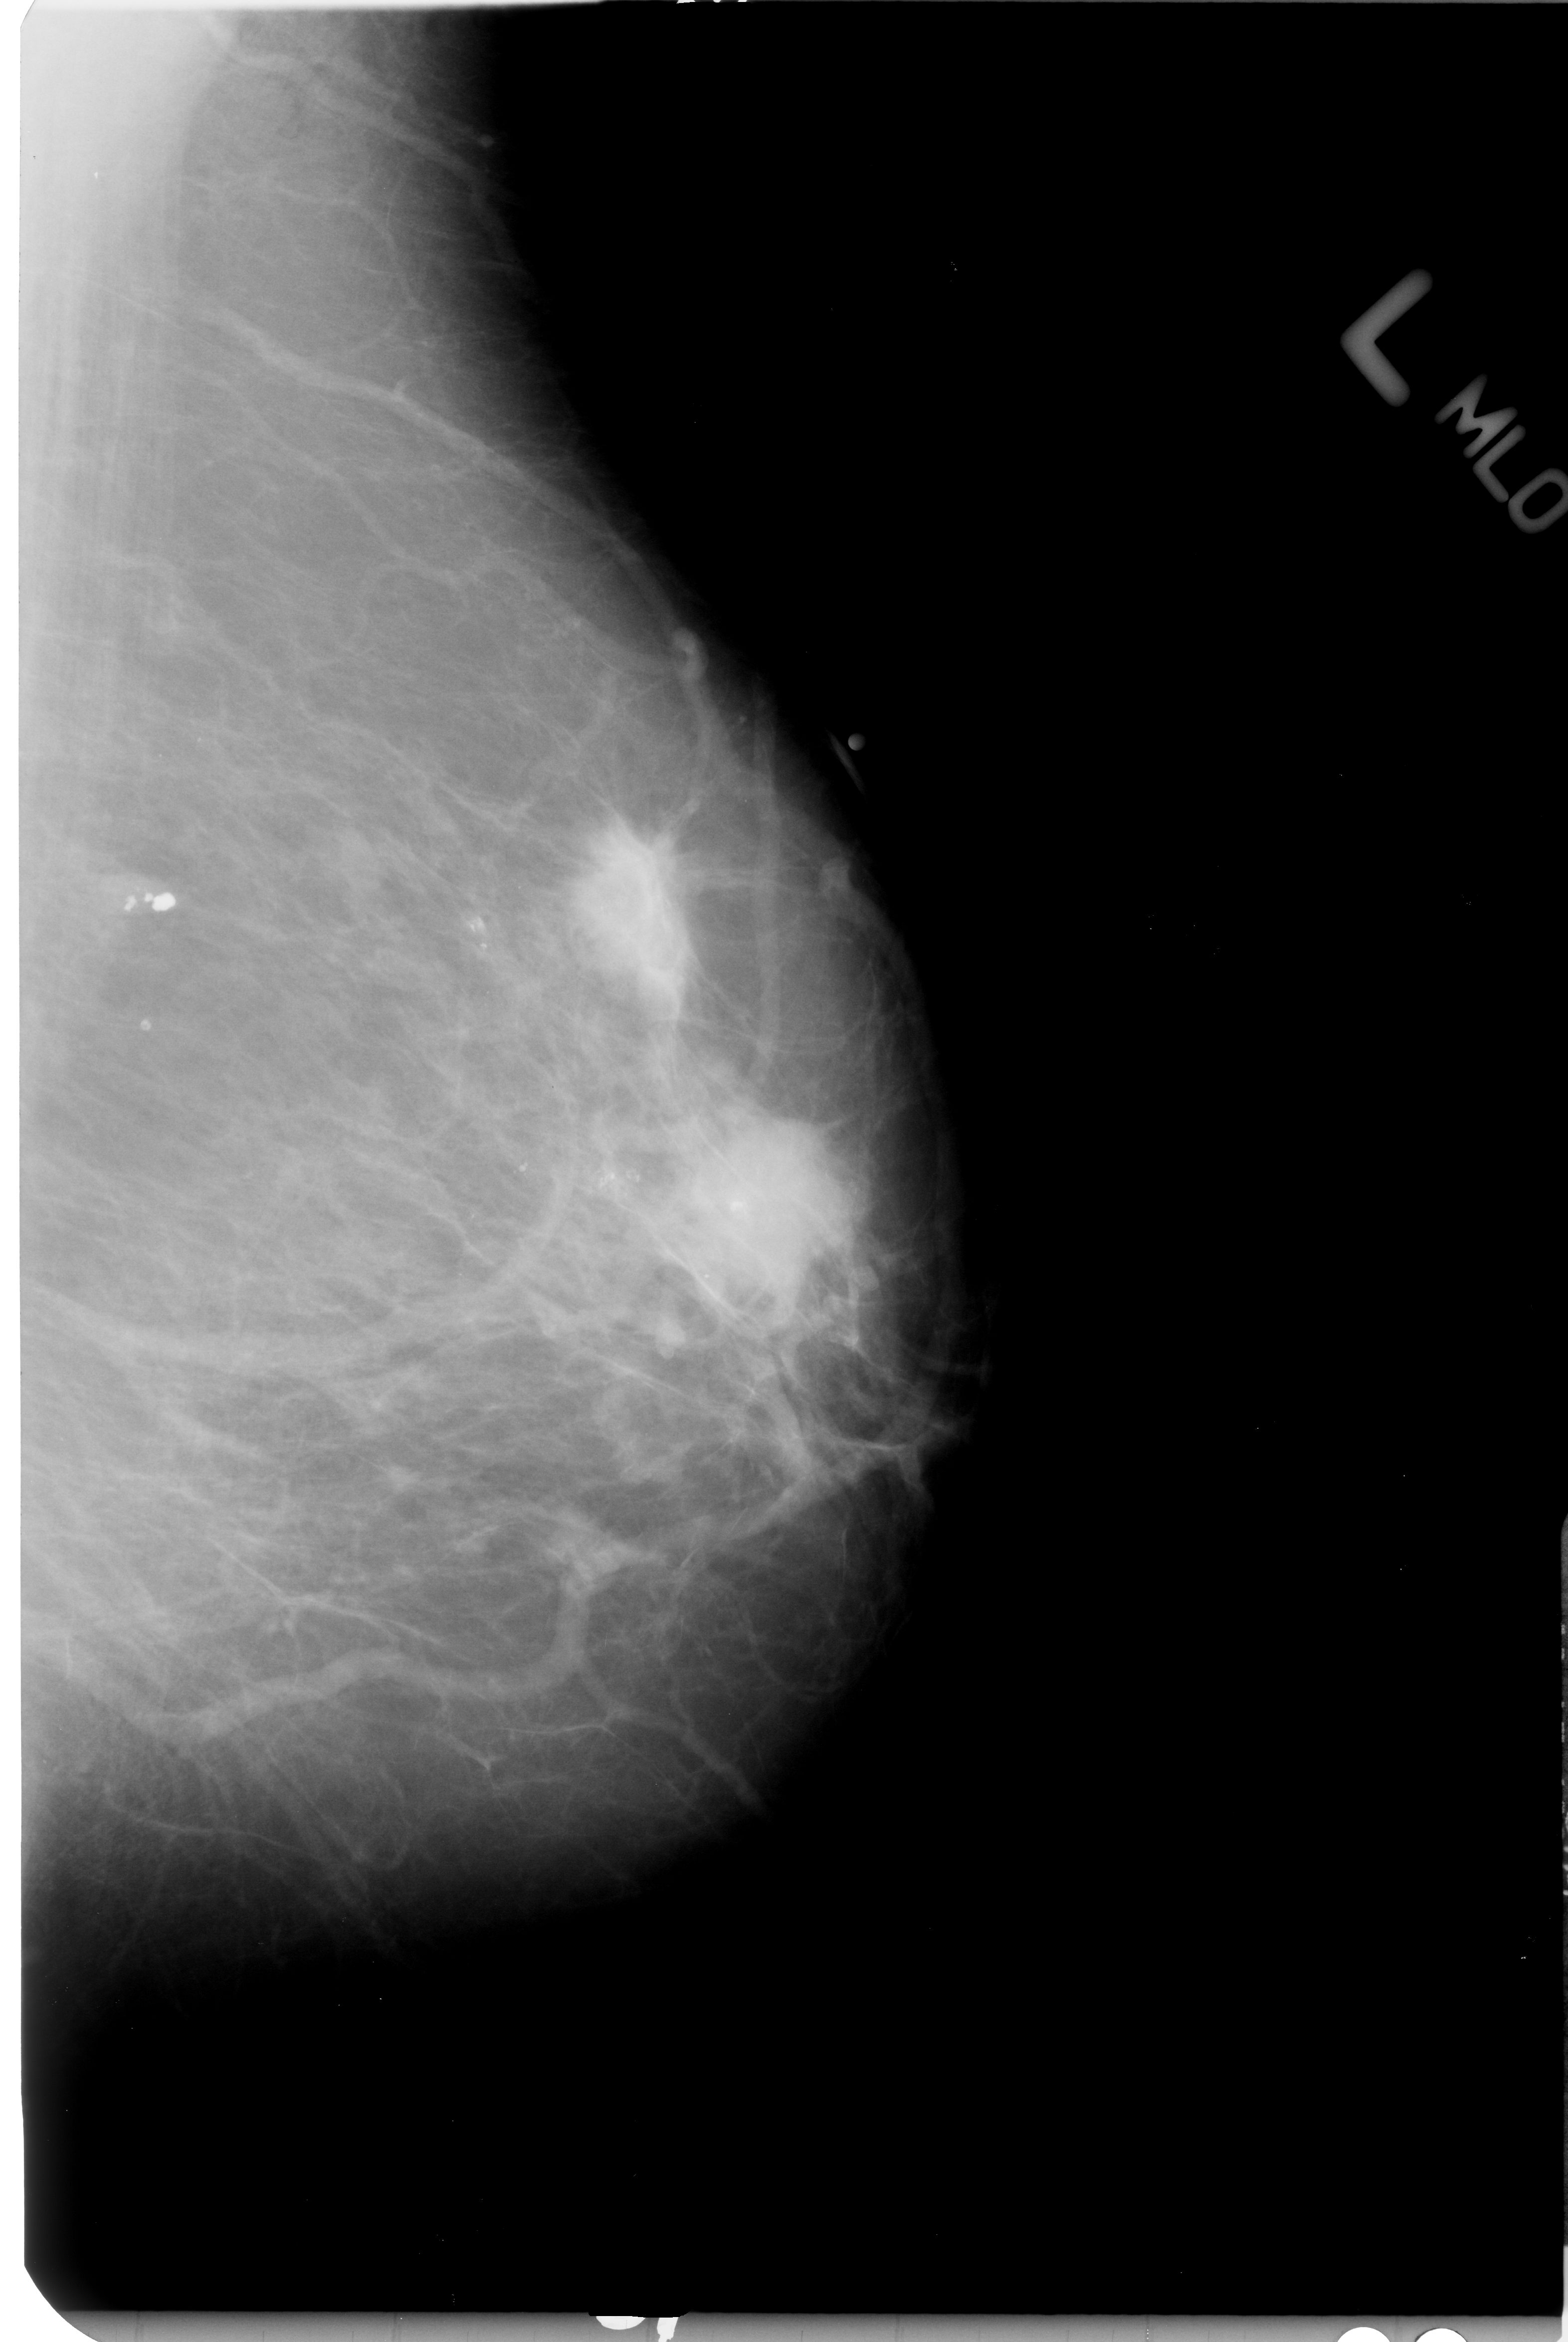
Digitized screen-film mammogram; left breast; MLO view; BI-RADS breast density category 2 (scale 1–4); 1568 × 2342 image matrix.
Expert-marked regions of interest on this film, with their recorded descriptors:
- Finding 1 of 2: mass, shape irregular / architectural distortion, margins spiculated; BI-RADS assessment category 5; subtlety rating 5 on a 1 (subtle) to 5 (obvious) scale; pathology result (as recorded, not read from the image): malignant: bounding box <560,800,714,991> (left, top, right, bottom; pixels)
- Finding 2 of 2: mass, shape irregular, margins ill defined / spiculated; BI-RADS assessment category 4; pathology (as recorded): malignant: <685,1101,890,1311>